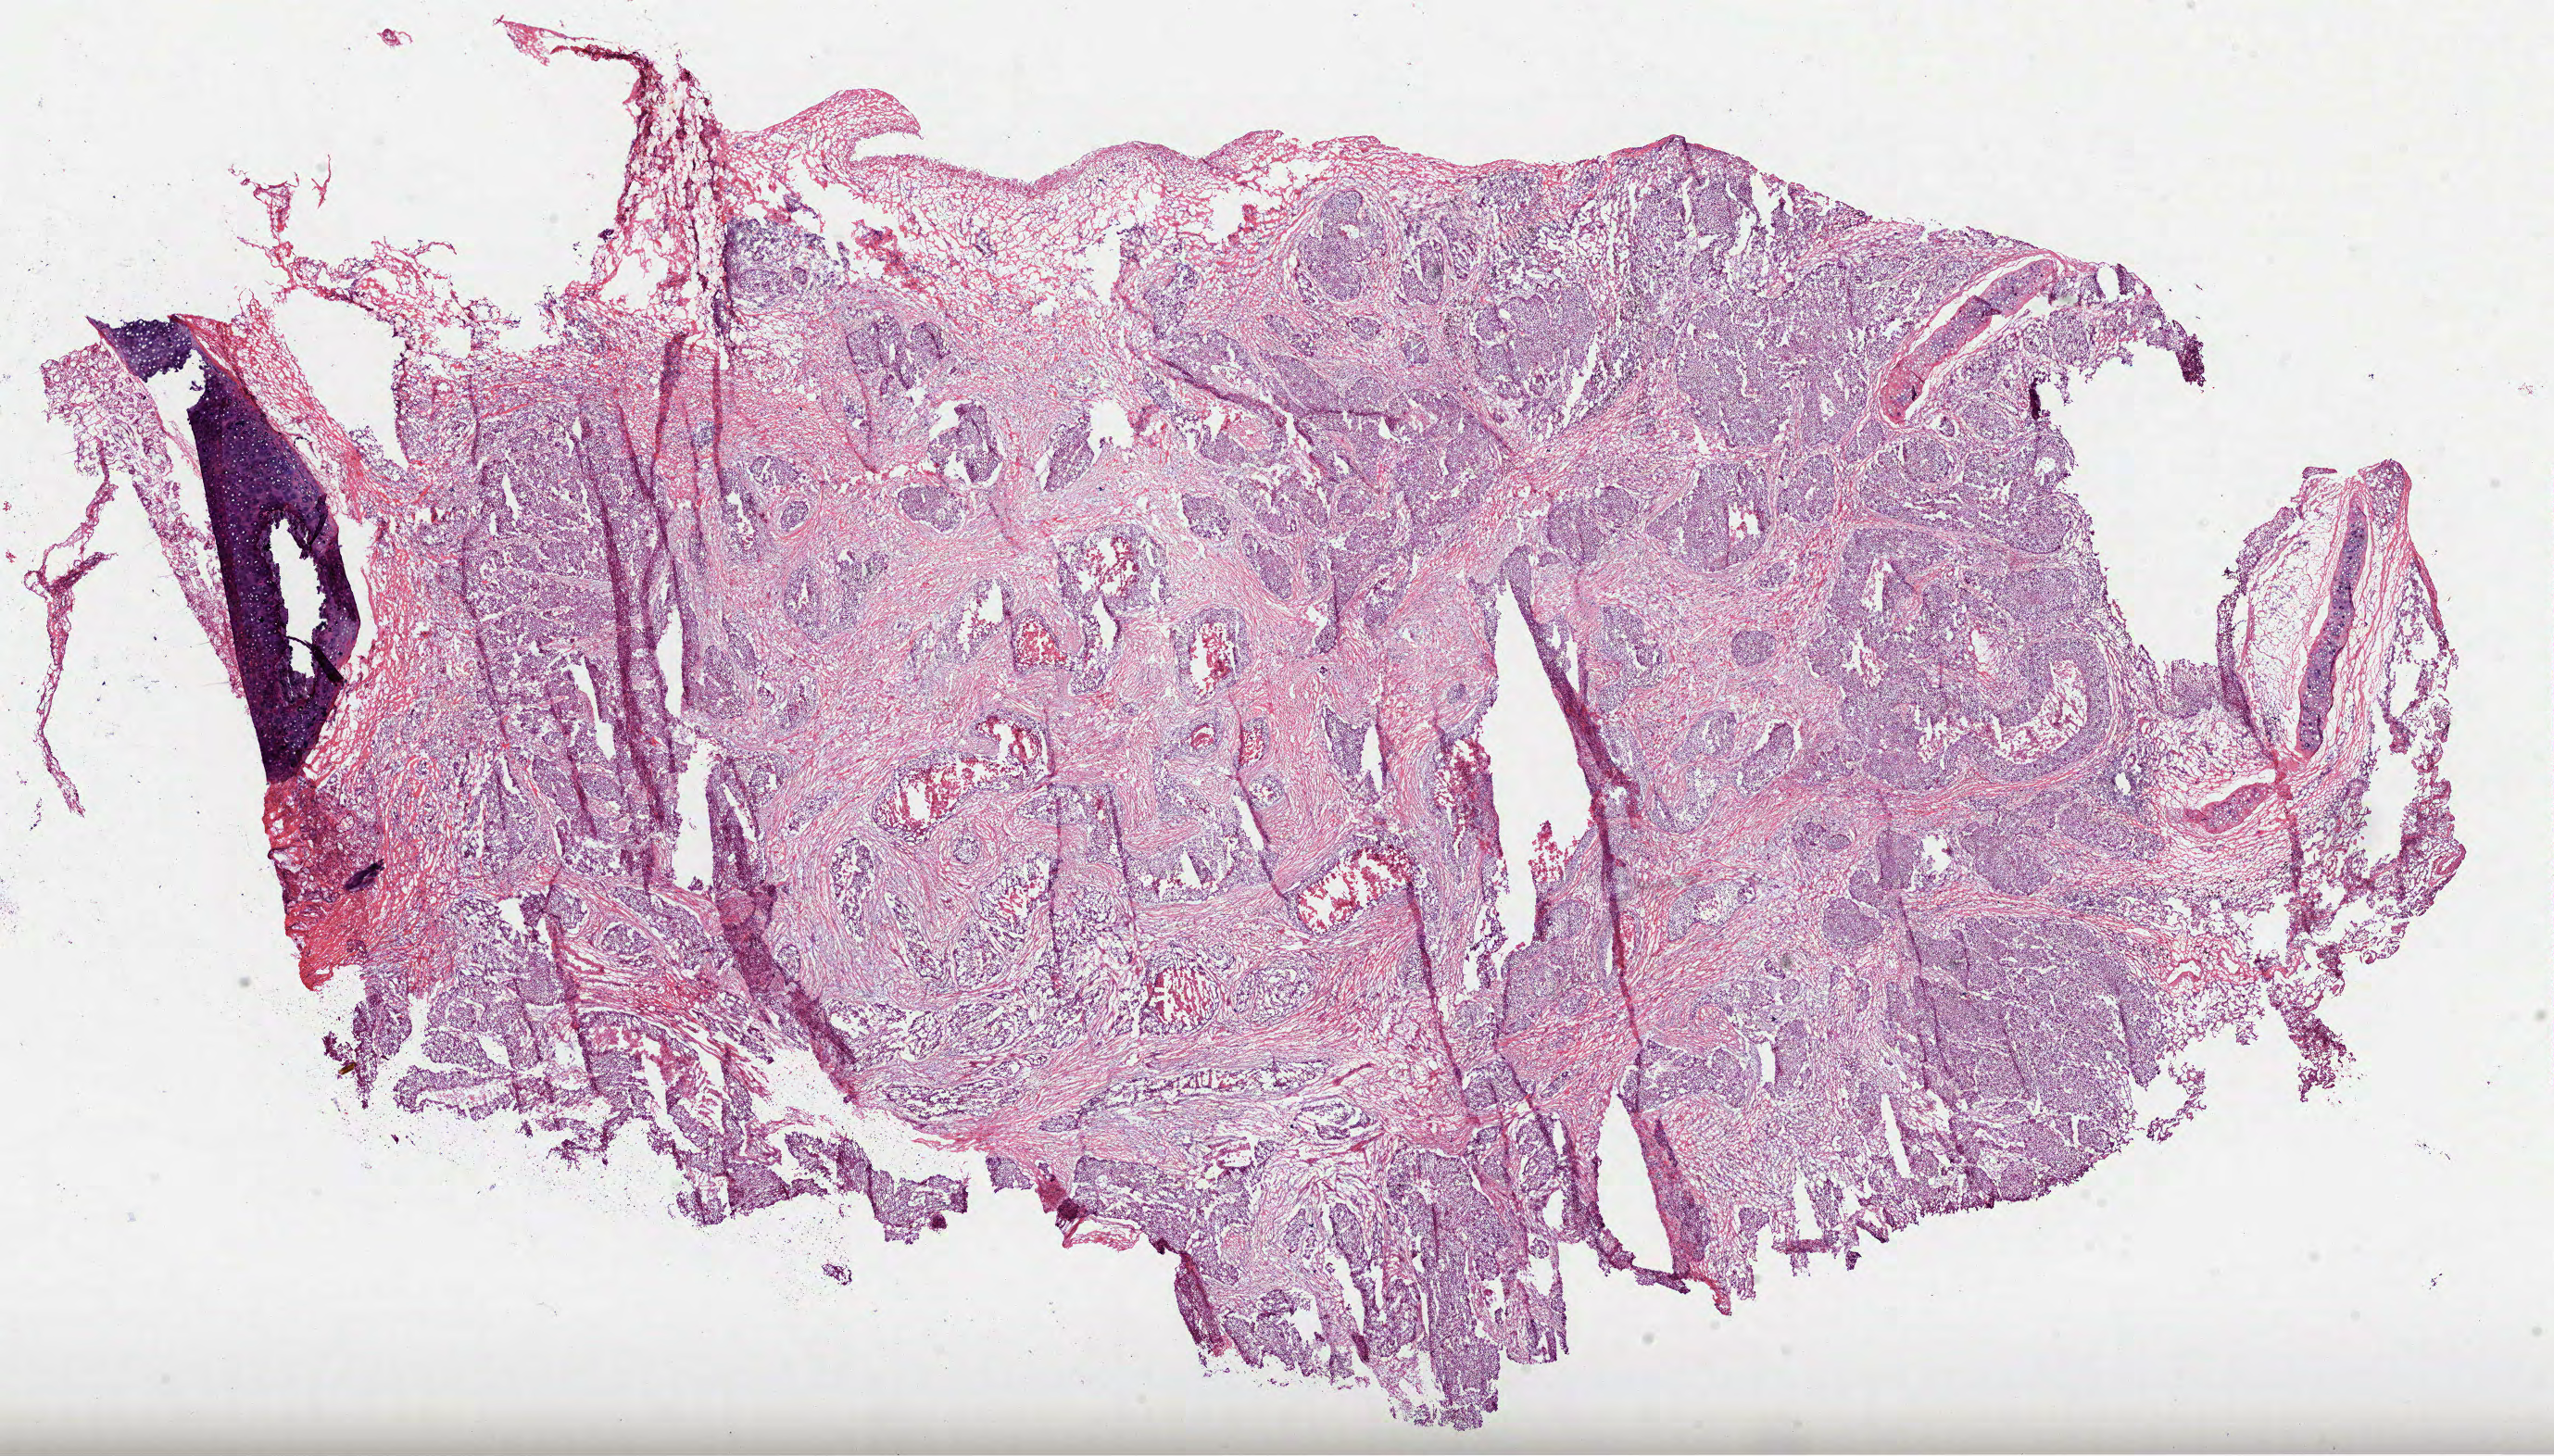
H&E-stained whole-slide image — a low-resolution overview of the entire scanned area, about 22.2 x 12.7 mm (acquisition: 40x scan). Frozen section. Primary tumour sample from the lung. Male patient; age at initial diagnosis 64 years. Slide review estimates, as recorded: tumour cells 60%, tumour nuclei 70%, normal cells 10%, stromal cells 22%, necrosis 8%. Inflammatory infiltration, as recorded: lymphocyte infiltration 5%.
* AJCC pathologic stage: IA
* laterality: left
* pathologic diagnosis: Squamous cell carcinoma, NOS (upper lobe, lung)